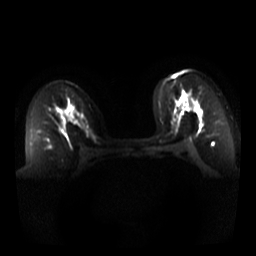
Breast MRI, one axial slice. Position 21 of 44 along the scan axis. Diffusion-weighted series; image 2 of 4 stored at this slice position (different b-values; order by instance number). 3 T. 5 mm slice thickness. 256 × 256 image matrix, field of view 340 × 340 mm. Female patient.
Annotated regions visible in this slice (outlined manually by an expert reader):
- tumour on diffusion-weighted imaging: bounding box [x1, y1, x2, y2] px = [182, 95, 197, 109]